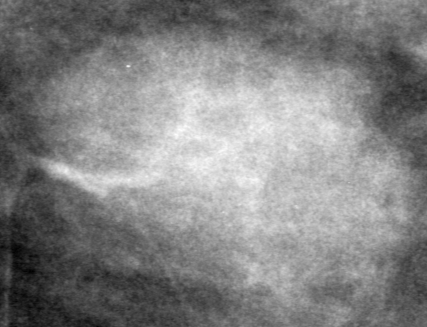
Crop from a digitized film mammogram around one marked abnormality; left breast; CC view; BI-RADS breast density category 2 (scale 1–4).
Finding: mass, shape oval, margins obscured; BI-RADS assessment category 0 (incomplete: needs additional imaging); subtlety rating 4 on a 1 (subtle) to 5 (obvious) scale; pathology (as recorded): benign.